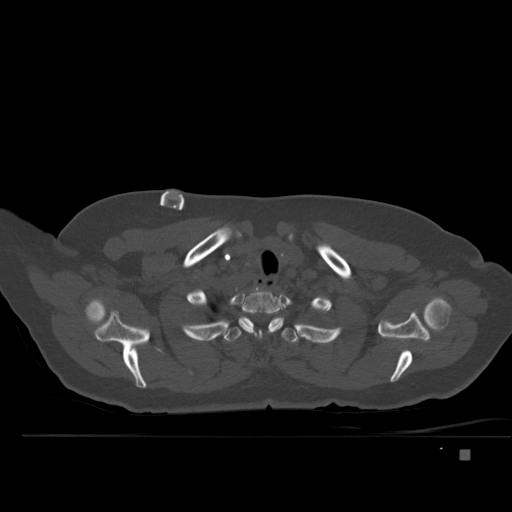
CT including the spine, one axial slice. Slice 398 of 477 in the series (ordered by position). Bone window (W 1800 / L 400 HU). 1.5 mm slice thickness. 512 × 512 image matrix, field of view 422 × 422 mm. Patient: female, 74 years. Case-level facts recorded for this patient, not image findings: primary cancer: colon.
Outlined on this slice (semi-automatically segmented with operator editing):
- T1 vertebra: box from (x=219, y=291) to (x=282, y=337) px
- T2 vertebra: (x=198, y=316)–(x=315, y=343)